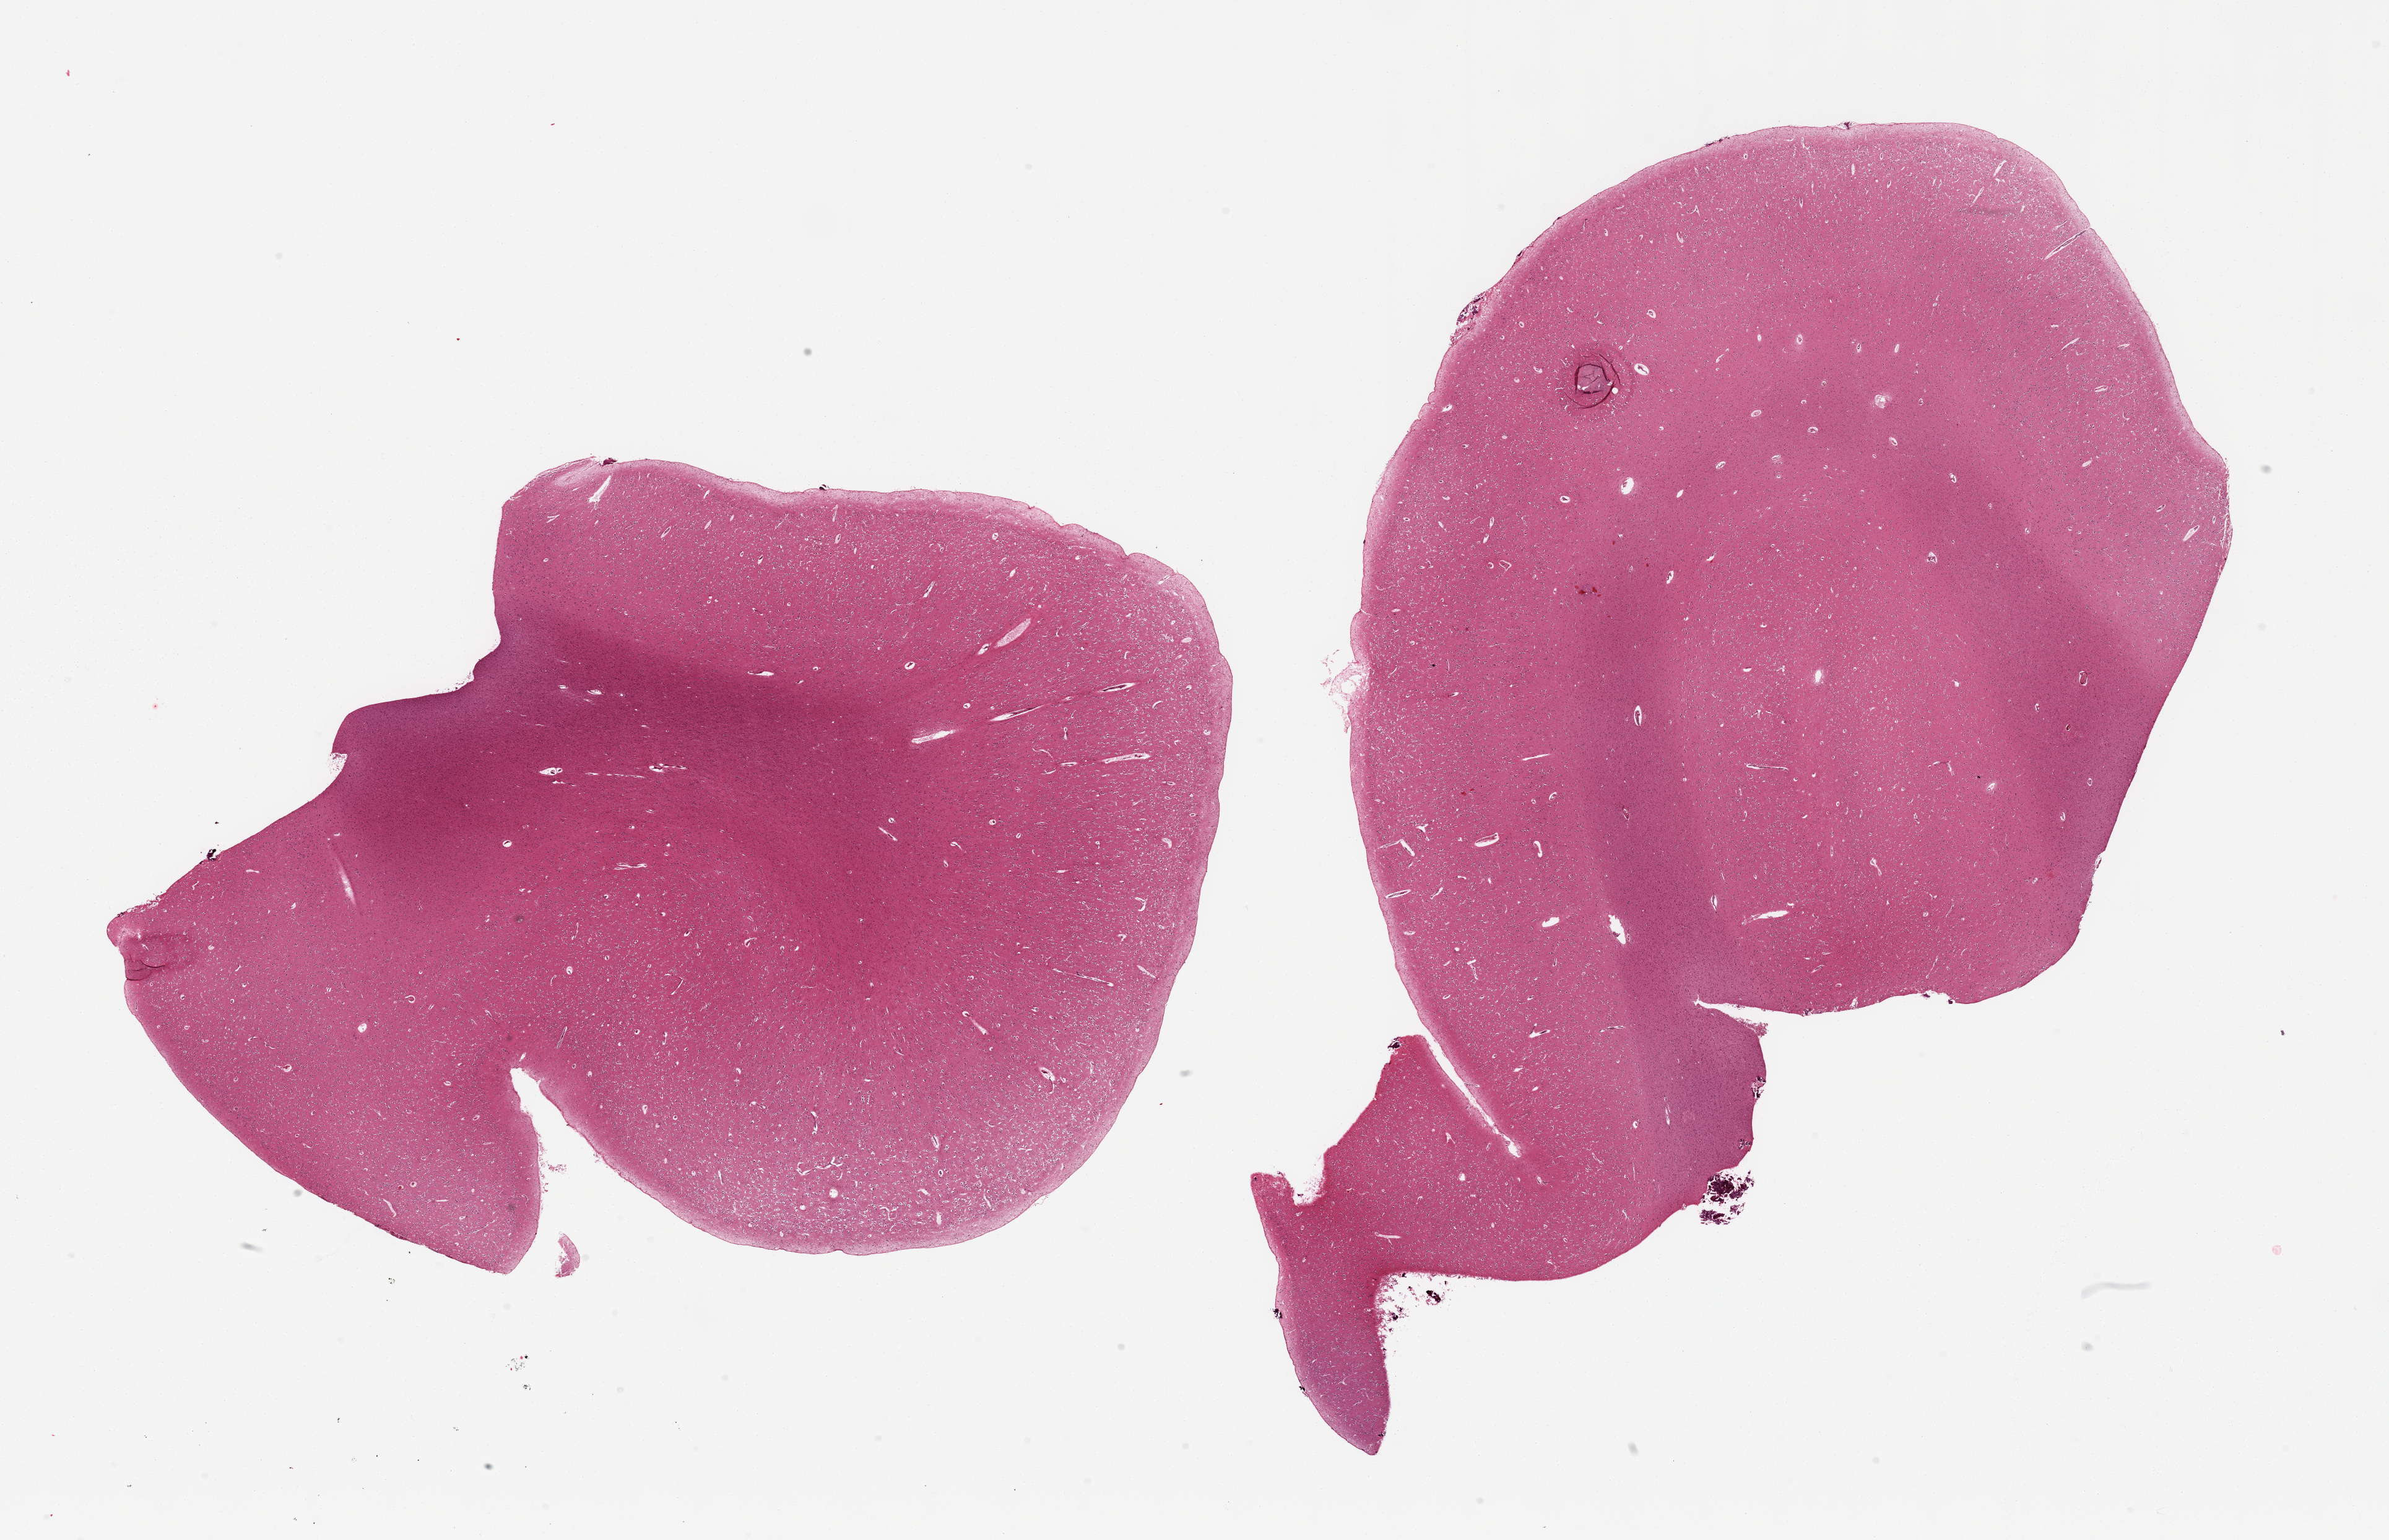
Hematoxylin and eosin (H&E) whole-slide image, a low-resolution overview of the entire scanned area, about 30.5 x 19.7 mm (from a 20x scan), PAXgene-fixed, paraffin-embedded tissue, target tissue: cerebral cortex, tissue donor sample. Donor: male.
- reviewer comment on this tissue sample: 2 pieces; numerous tiny 0.2mm surface calcifications; may be bone 'dust' from sawing